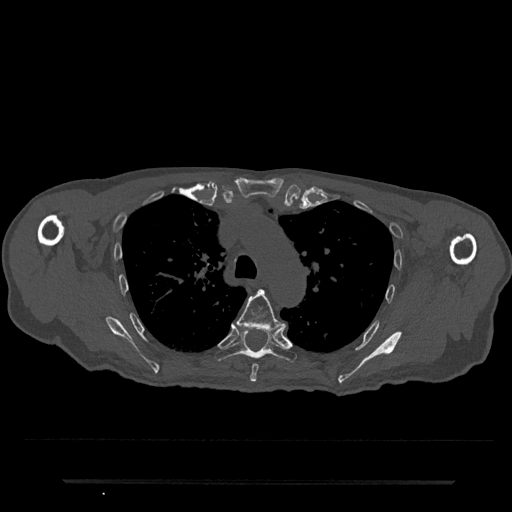
CT including the spine, one axial slice. Reconstruction kernel Br40s/3. Bone window (W 1800 / L 400 HU). 0.5 mm slice thickness. 512 × 512 image matrix, field of view 427 × 427 mm. Male patient, age 74 years. From the clinical record (not read from this slice): primary cancer: prostate.
Structures marked on this image (semi-automatically segmented with operator editing):
- T5 vertebra: bounding box <236,289,287,382> (left, top, right, bottom; pixels)
- T6 vertebra: <214,329,297,363>